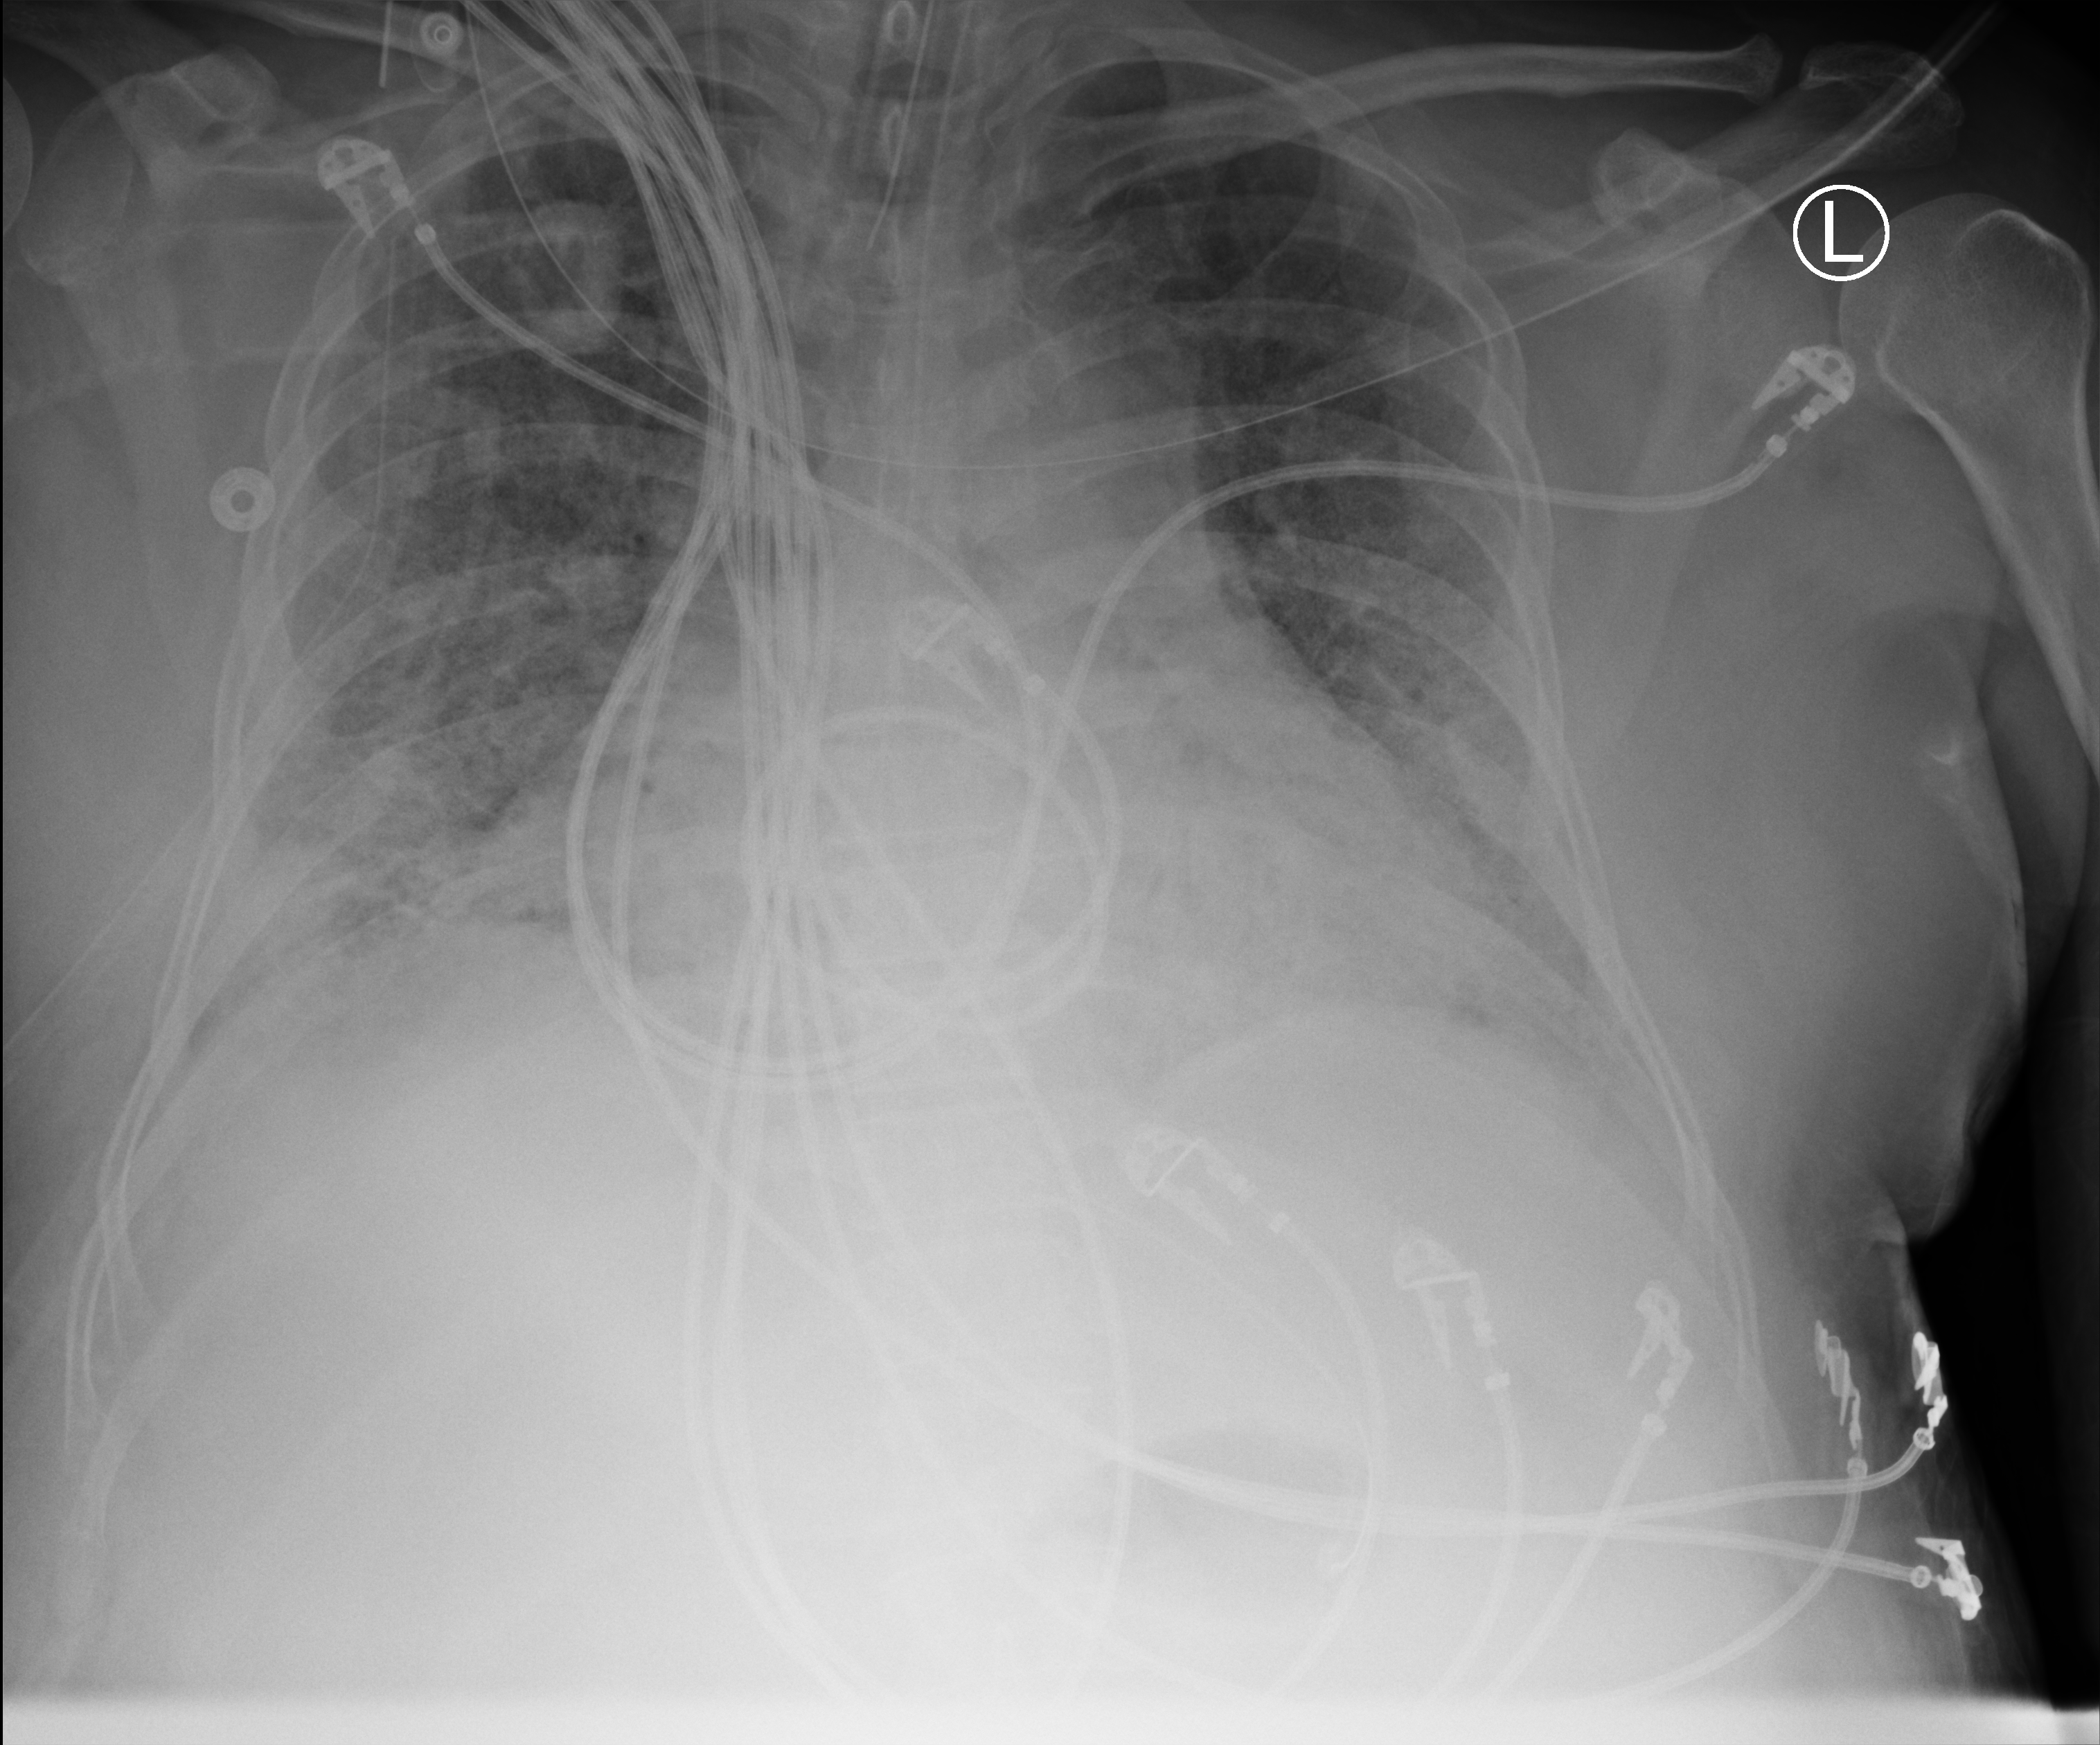
Bedside chest radiograph (computed radiography). Patient hospitalised with COVID-19, aged 18–59 years.
From the hospital-stay record, not from the radiograph (when in the stay this image was taken is not recorded): length of hospital stay: 48 days.